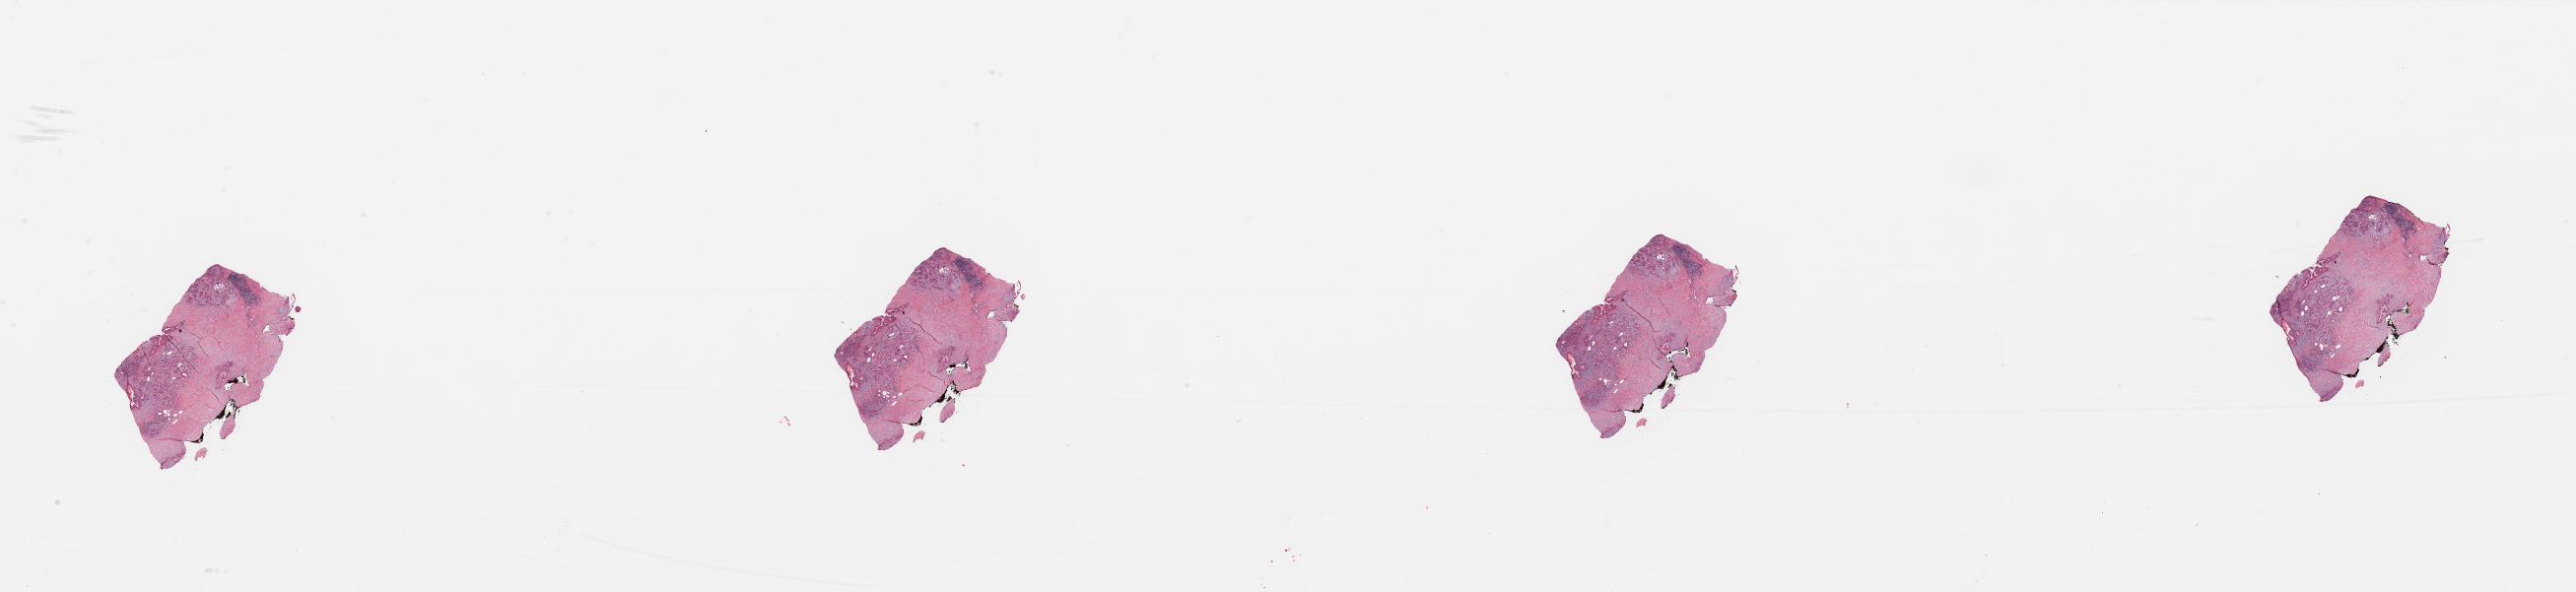
Digitized H&E tissue section (whole slide) — shown as a low-resolution overview of the whole scanned area (about 41.3 x 9.5 mm, from a 20x scan); tumour tissue sample, sampled site: pancreas. 66-year-old male patient. Histologic grade: G2 (moderately differentiated). Composition of this section per pathologist review: tumour nuclei 20%, necrosis 0%.
Primary tumour site (as recorded): head. Diagnosis: Infiltrating duct carcinoma, NOS. AJCC pathologic stage: IIB.